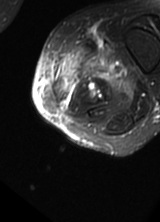
MRI of an extremity soft-tissue mass, one axial slice; position 10 of 69 along the scan axis; T2-weighted fat-saturated; MR volume resampled by the dataset authors to the PET/CT grid (not the native acquisition matrix); 3.27 mm slice thickness; 160 × 222 image matrix. Female patient. Case-level facts recorded for this patient, not image findings: histological type: pleomorphic leiomyosarcoma; grade: high; site of the primary tumour: left thigh.
Annotated regions visible in this slice (expert contour drawn on MRI and transferred to this co-registered scan by the dataset authors):
- gross tumour volume including surrounding oedema: bounding box <52,36,135,108> (left, top, right, bottom; pixels)